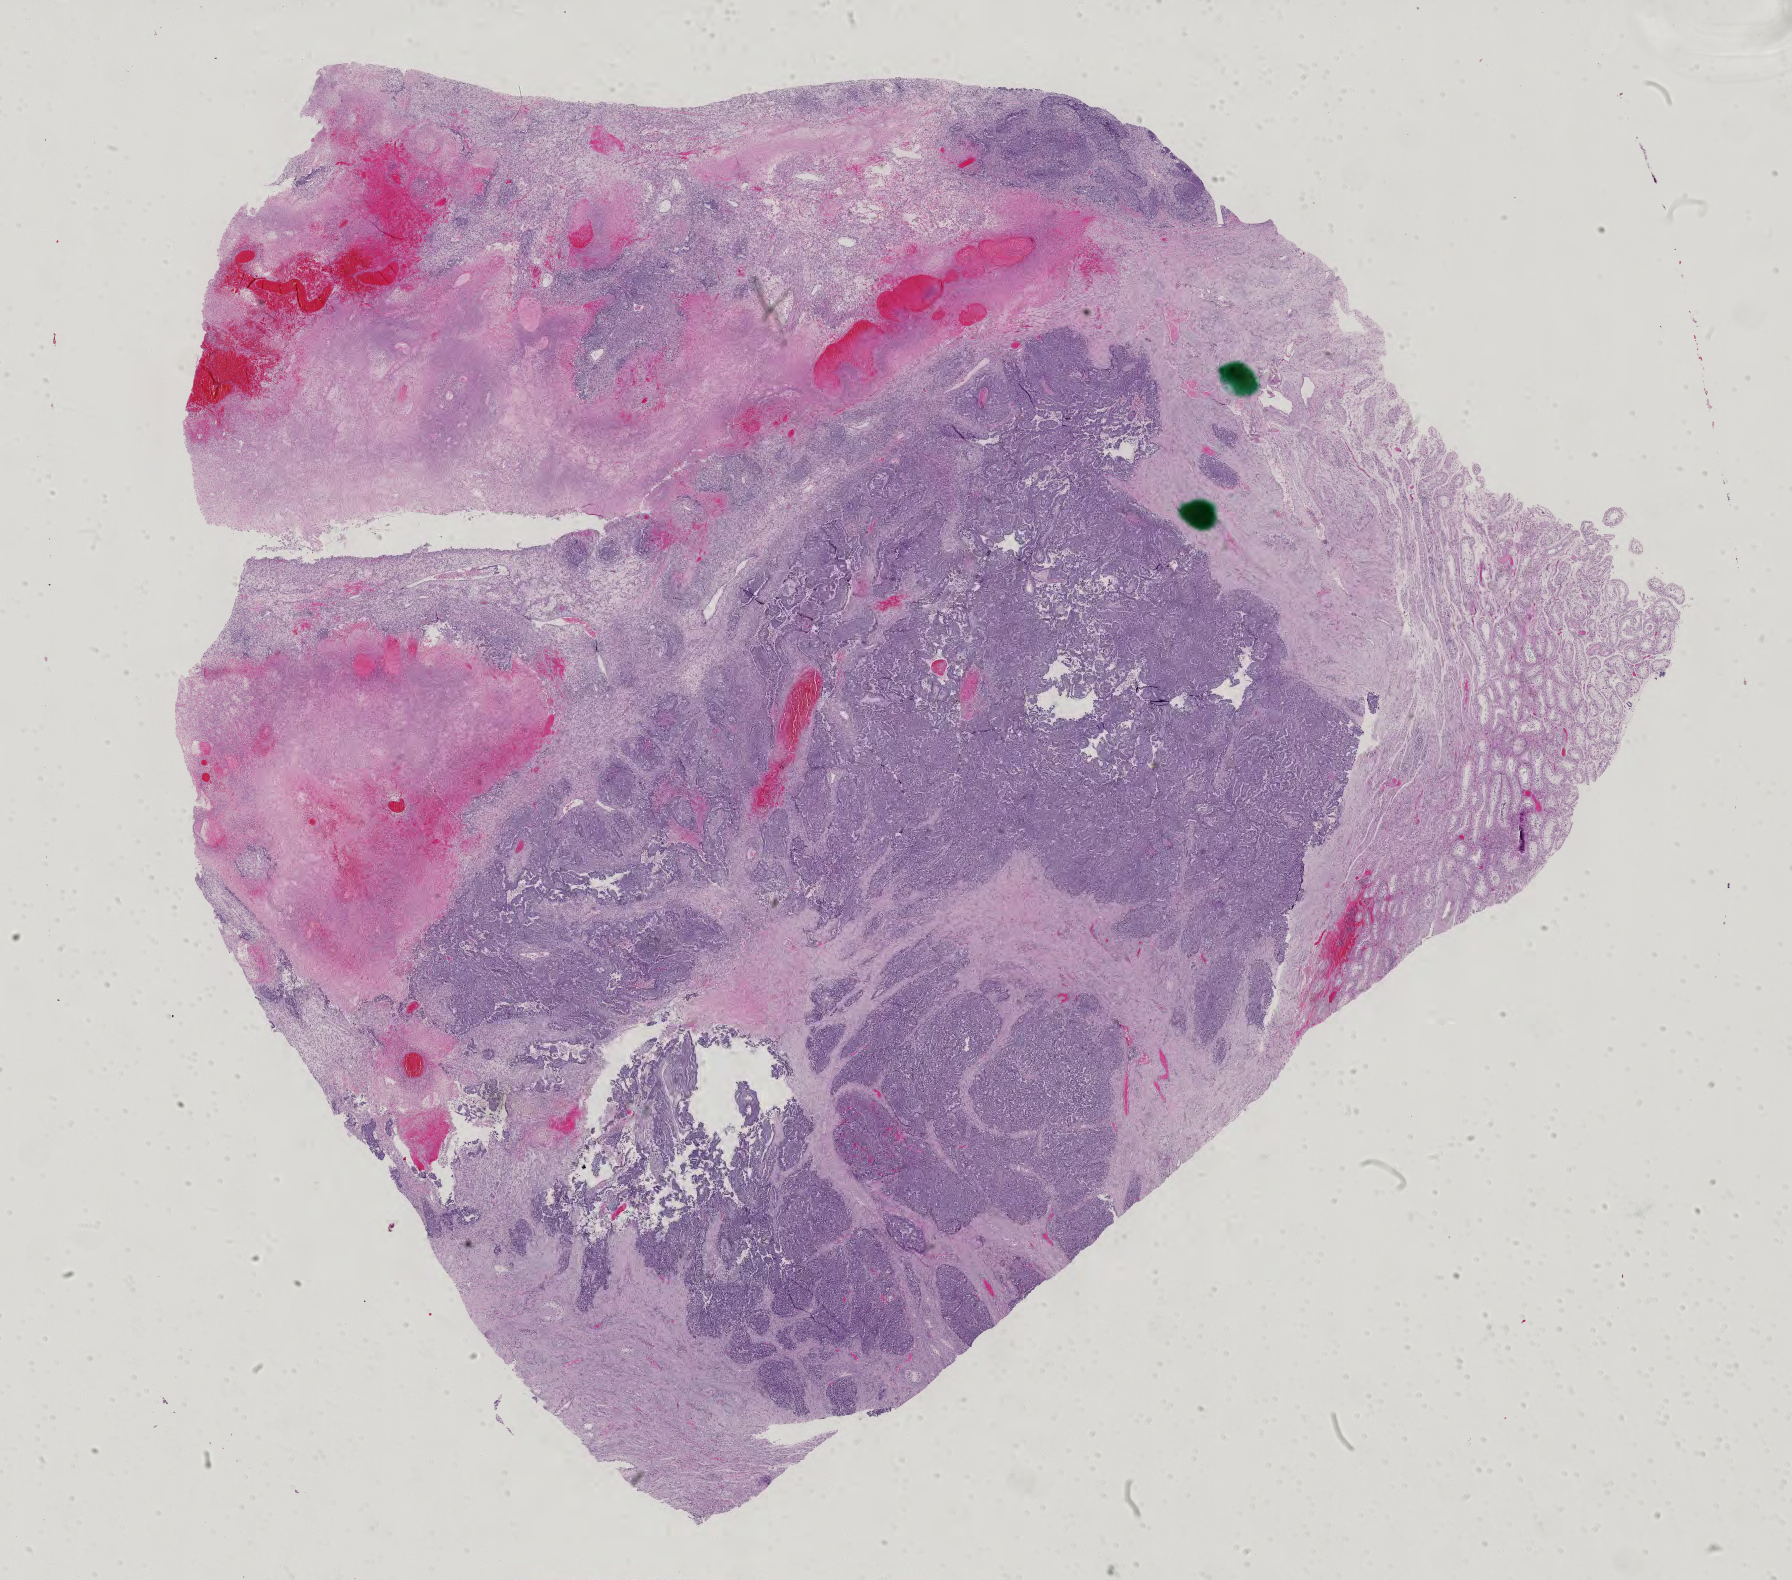
Digitized Hematoxylin and eosin (H&E) stained tissue section (whole slide), low-resolution overview of the scanned area, about 26.1 x 23.0 mm; formalin-fixed paraffin-embedded (FFPE) diagnostic section; primary tumour sample from the testis. Patient: male, age at initial diagnosis 26 years.
AJCC pathologic stage: IIIB. Diagnosis: Embryonal carcinoma, NOS.